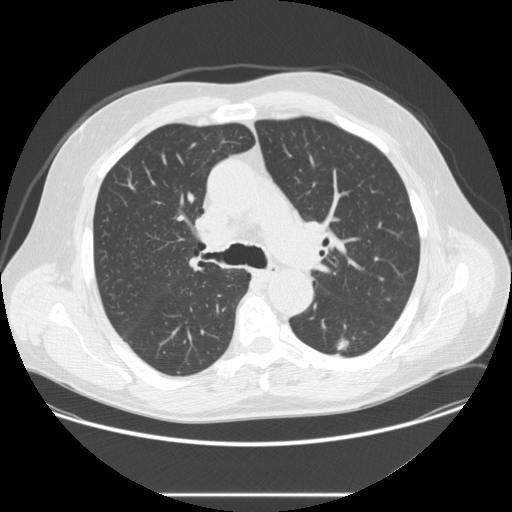
Low-dose screening chest CT, one axial slice. Position 167 of 262 along the scan axis. 120 kVp. Lung window (W 1500 / L -600 HU). 2.5 mm slice thickness. 512 × 512 image matrix, field of view 420 × 420 mm.
Annotated regions visible in this slice (expert manual segmentation):
- lesion 1 (tumor, lower lobe of left lung): bounding box [x1, y1, x2, y2] px = [337, 338, 349, 350]